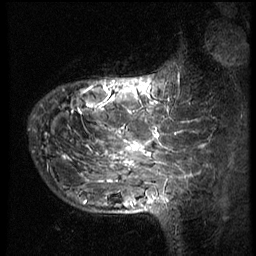
Breast MRI (dynamic contrast-enhanced), one sagittal slice. Position 18 of 66 along the scan axis. 3 images stored at this slice position (order not interpretable as contrast timing). 1.5 T. TE 4.2 ms, TR 8.9 ms. 2.5 mm slice thickness. 256 × 256 image matrix, field of view 200 × 200 mm. Patient: female, 39 years. Case-level facts recorded for this patient, not image findings: setting: breast cancer imaged before/during neoadjuvant chemotherapy; receptor status: HER2-positive.
Outlined on this slice (semi-automatically segmented with operator editing):
- analysis volume of interest (the breast-tissue region the enhancement analysis was run in; not a lesion): bounding box (x1, y1, x2, y2) in pixels: (29, 57, 166, 196)
- tumour enhancement mask (voxels above the 140 % enhancement threshold inside the analysis volume of interest): (63, 81, 159, 166)